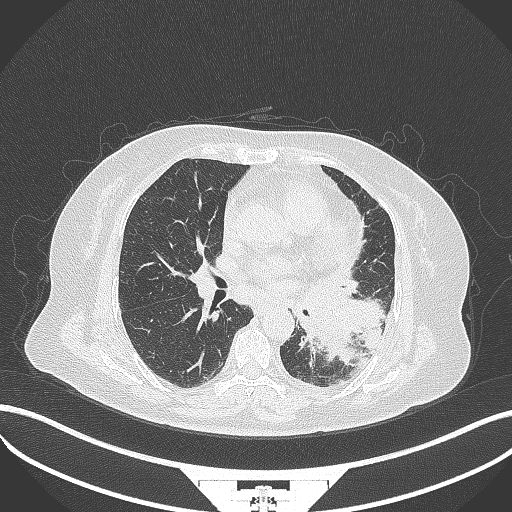
Chest CT, one axial slice; slice 175 of 322 in the series (ordered by position); lung window (W 1500 / L -600 HU); 1 mm slice thickness; 512 × 512 image matrix. Patient: female, 69 years. From the clinical record (not read from this slice): clinical TNM (as recorded): T2b N3 M1.
Outlined on this slice (rectangle marked by the reading radiologist):
- lung tumour (recorded histology: adenocarcinoma): box from (x=301, y=282) to (x=386, y=371) px